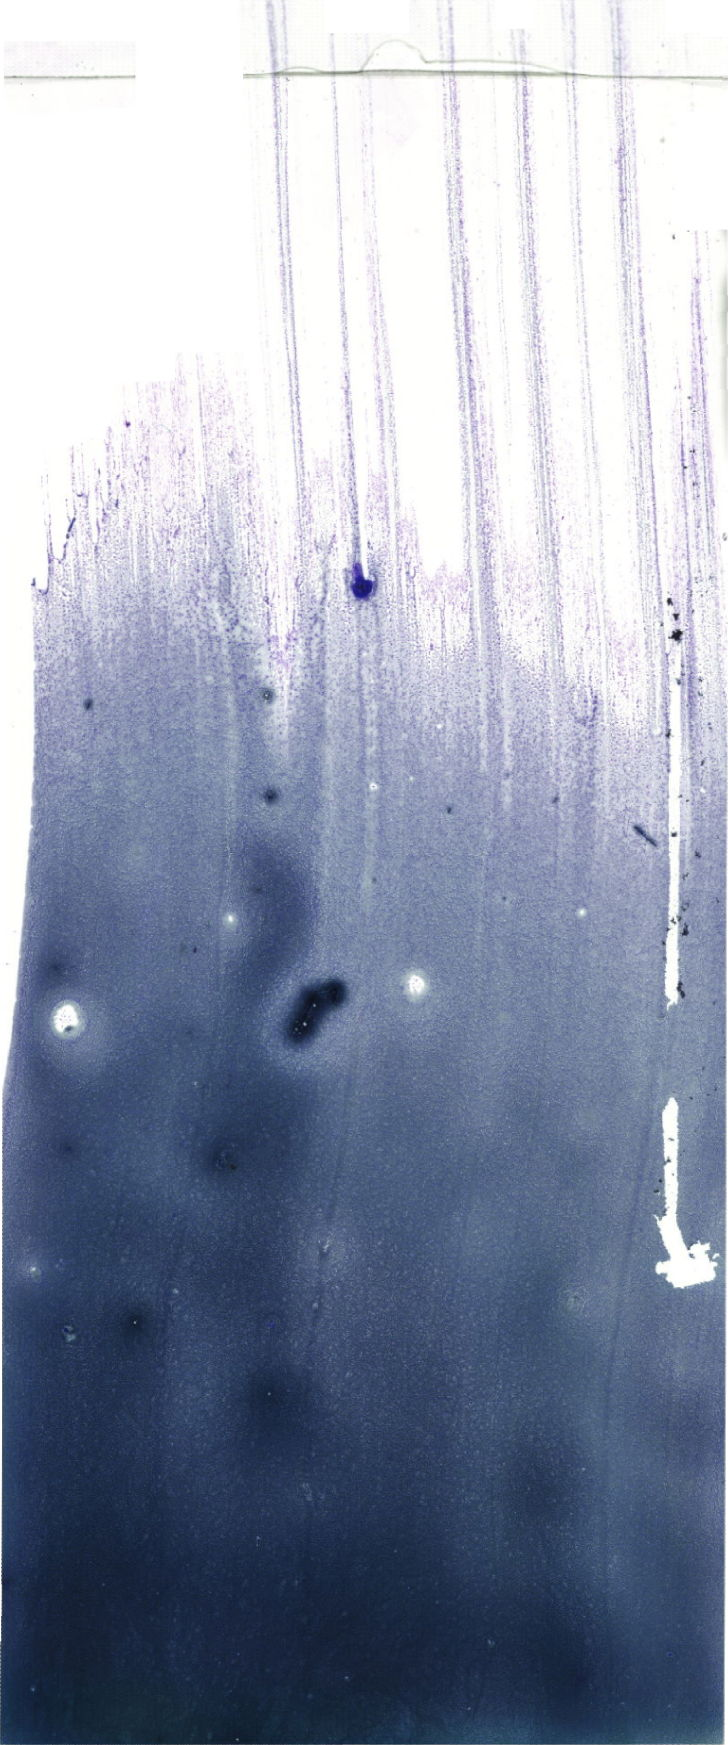
May-Grünwald-Giemsa (MGG)-stained marrow aspirate smear (whole slide), shown as a low-resolution overview of the whole scanned area (about 20.6 x 49.5 mm). Male patient.
* diagnosis: T Acute Lymphoblastic Leukemia